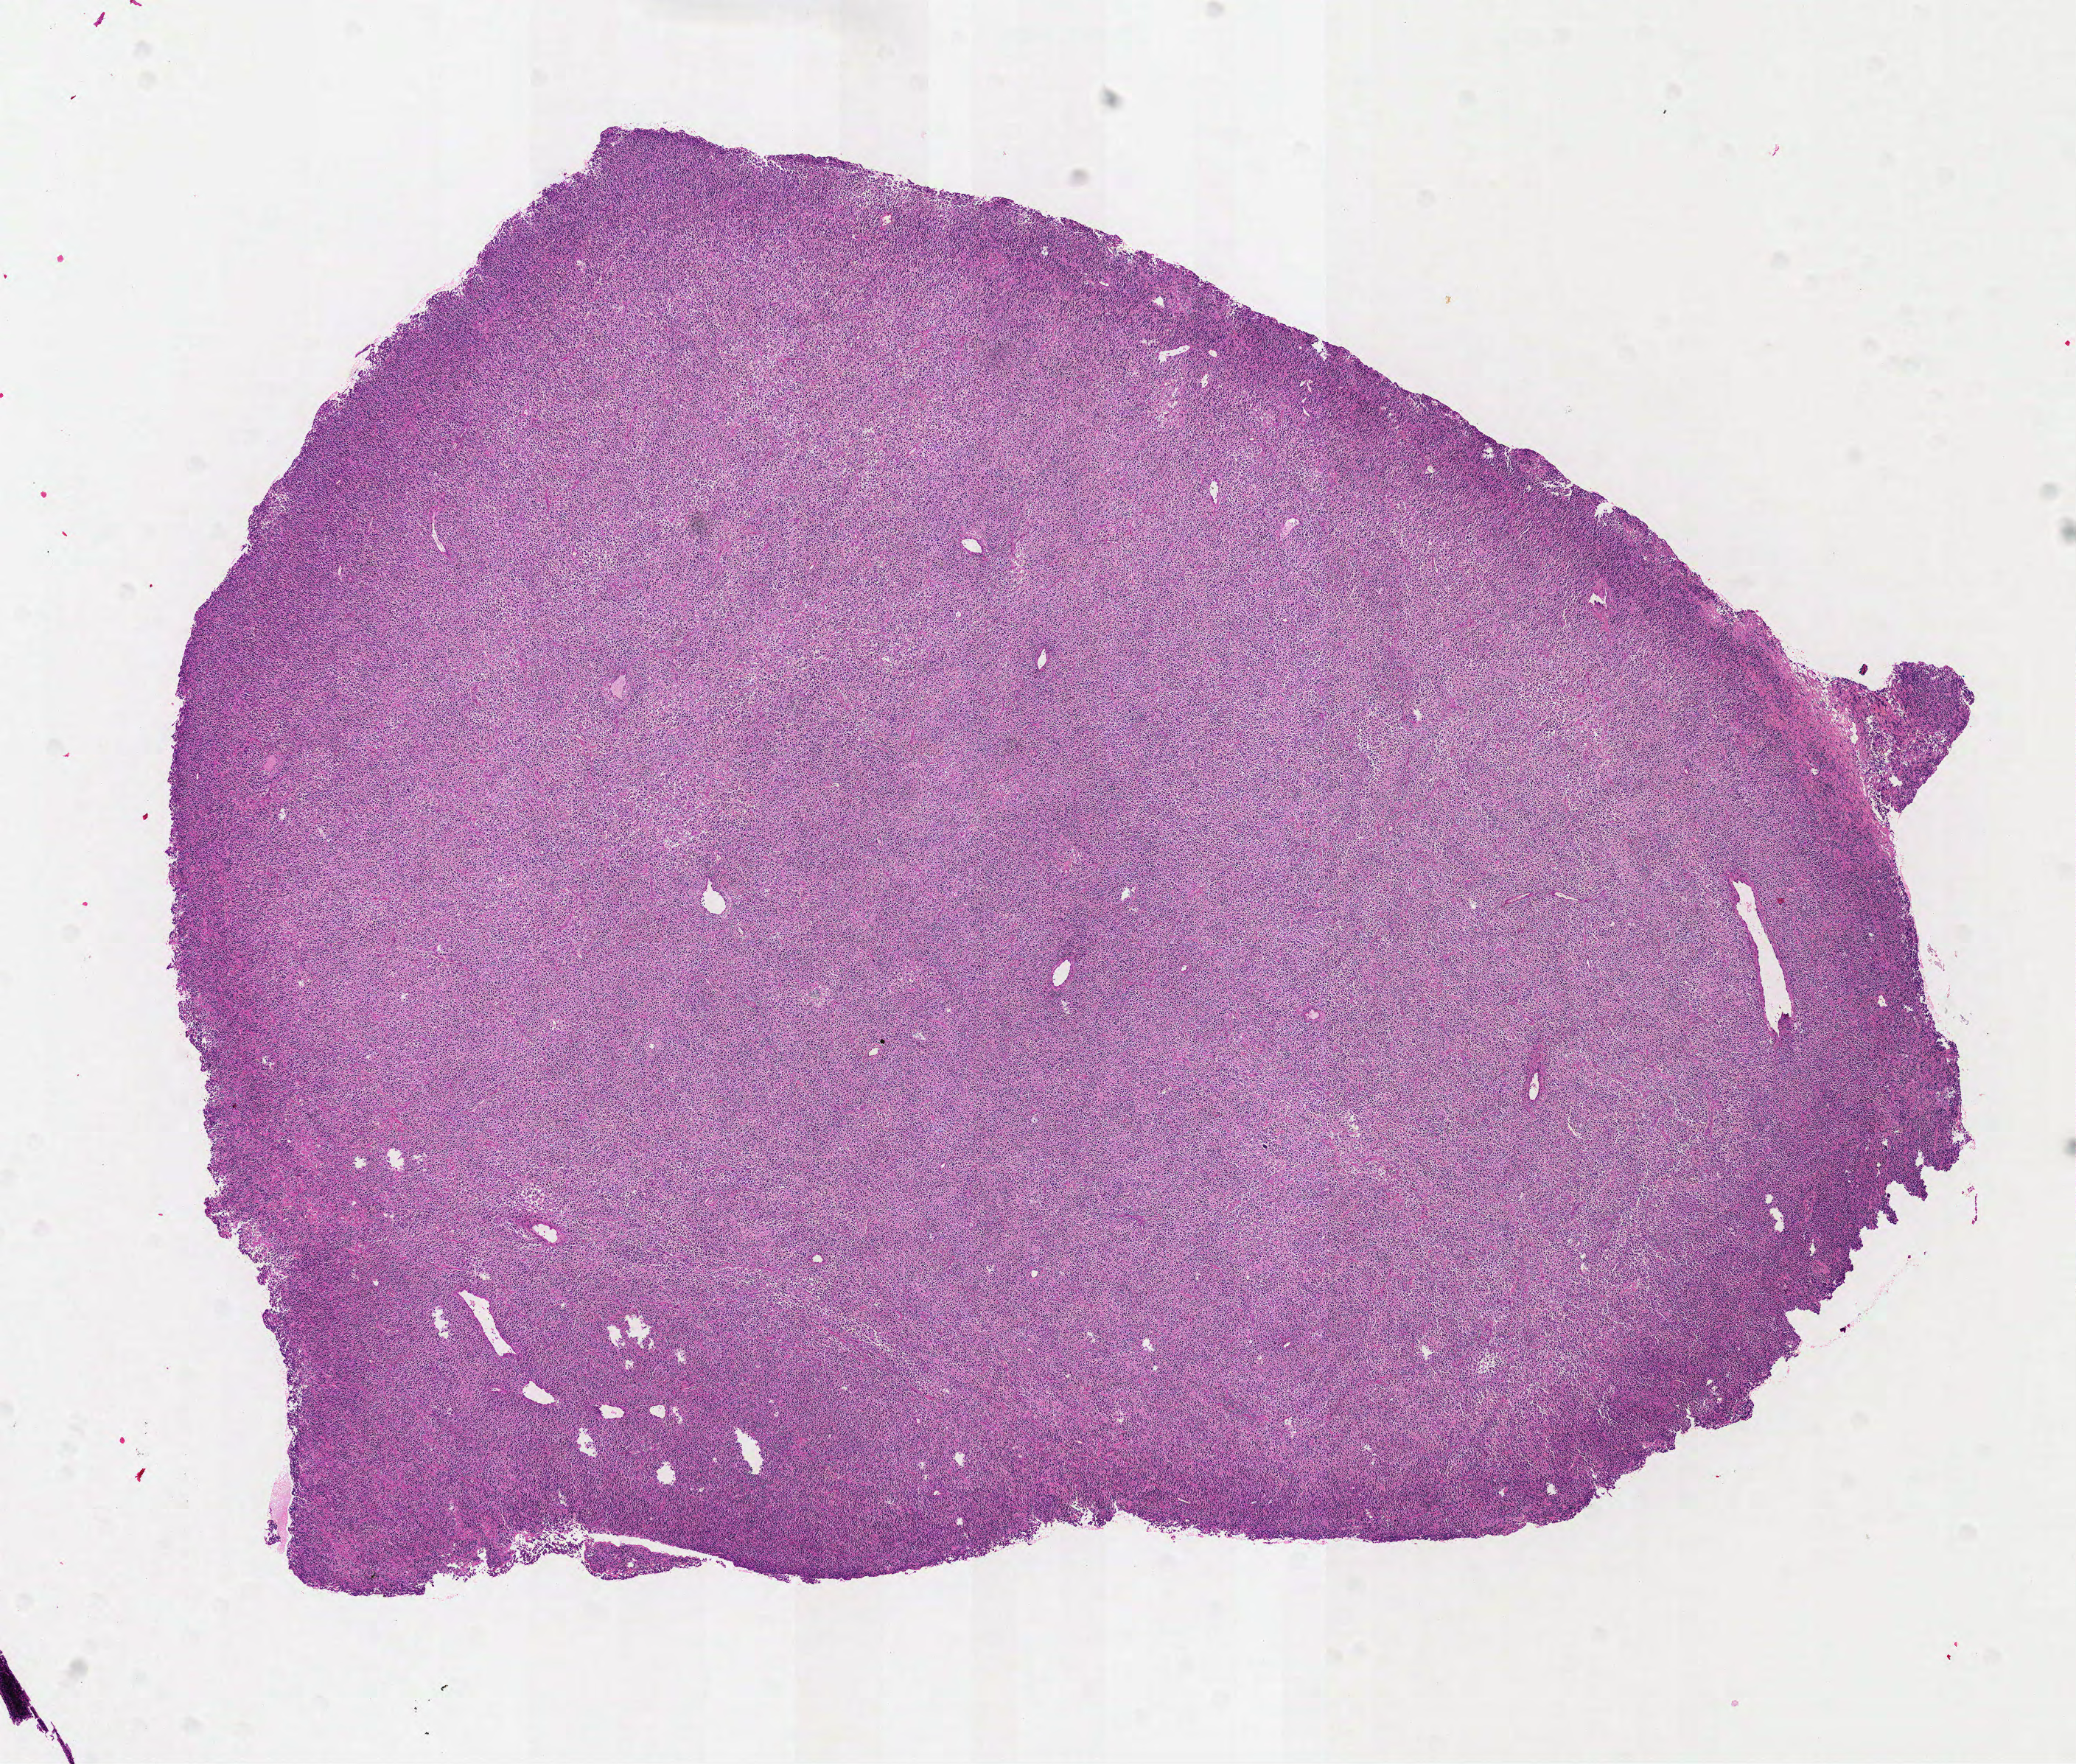
Whole-slide histology image, H&E — shown as a low-resolution overview of the whole scanned area (about 11.4 x 9.7 mm); formalin-fixed paraffin-embedded (FFPE) diagnostic section; sample: primary tumour, lymphoid tissue. Female patient; age at initial diagnosis 28 years.
Diagnosis: Mediastinal (thymic) large B-cell lymphoma (anterior mediastinum).